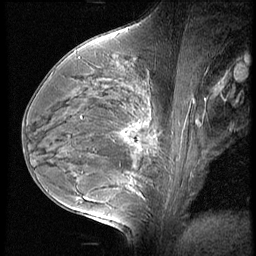
Breast MRI (dynamic contrast-enhanced), one sagittal slice; slice 33 of 60 in the series (ordered by position); 3 images stored at this slice position (order not interpretable as contrast timing); 1.5 T; TE 4.2 ms, TR 9 ms; 2.5 mm slice thickness; 256 × 256 image matrix. Female patient, age 35 years. Case-level facts recorded for this patient, not image findings: setting: breast cancer imaged before/during neoadjuvant chemotherapy; receptor status: HR-positive, HER2-negative.
Outlined on this slice (semi-automatically segmented with operator editing):
- analysis volume of interest (the breast-tissue region the enhancement analysis was run in; not a lesion): bounding box (x1, y1, x2, y2) in pixels: (56, 58, 176, 202)
- tumour enhancement mask (voxels above the 140 % enhancement threshold inside the analysis volume of interest): (126, 128, 157, 151)